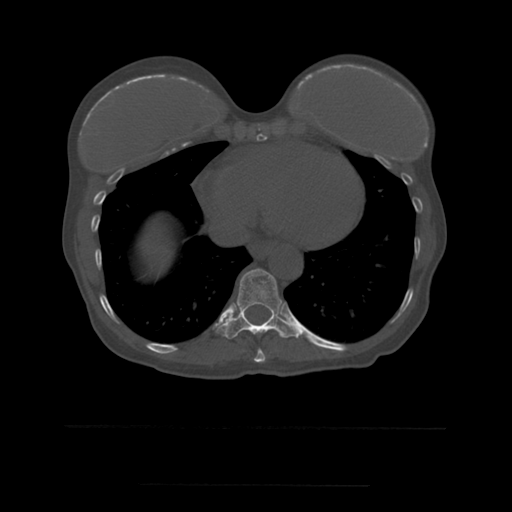
CT including the spine, one axial slice; slice 305 of 544 in the series (ordered by position); bone window (W 1800 / L 400 HU); 1.25 mm slice thickness; 512 × 512 image matrix. Patient age 58 years. From the clinical record (not read from this slice): primary cancer: lung.
Structures marked on this image (semi-automatic segmentation, software-assisted and operator-edited):
- T10 vertebra: box from (x=217, y=269) to (x=298, y=339) px
- T9 vertebra: (x=254, y=349)–(x=266, y=363)